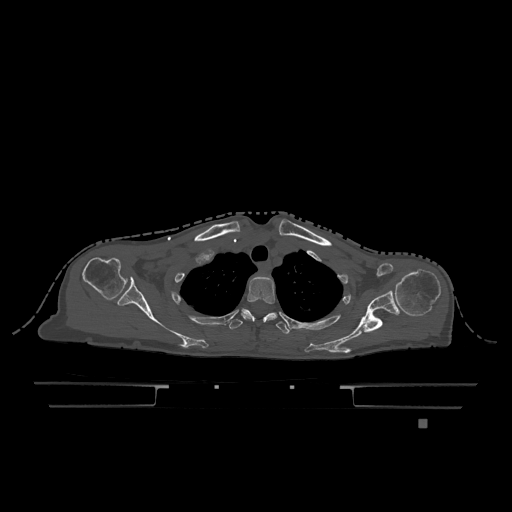
CT including the spine, one axial slice. Slice 949 of 1317 in the series (ordered by position). Bone window (W 1800 / L 400 HU). 0.5 mm slice thickness. 512 × 512 image matrix. Patient: female, 74 years. From the clinical record (not read from this slice): primary cancer: lung; vertebrae with lytic lesions (as recorded): T1, T4, T5, T6, L4, L5.
Structures marked on this image (semi-automatic segmentation, software-assisted and operator-edited):
- T2 vertebra: bounding box [x1, y1, x2, y2] px = [241, 276, 275, 321]
- T3 vertebra: [229, 309, 290, 334]
- T6 vertebra: [254, 313, 277, 321]